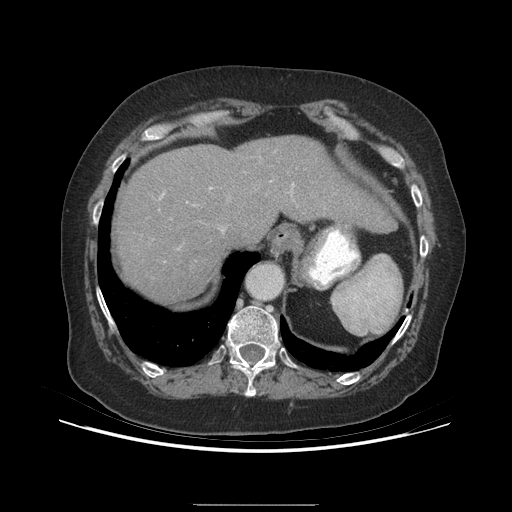
Contrast-enhanced abdominal CT (liver protocol), one axial slice. Slice 173 of 192 in the series (ordered by position). Reconstruction kernel STANDARD. 140 kVp. Soft-tissue window (W 400 / L 40 HU). 2.5 mm slice thickness. 512 × 512 image matrix. From the clinical record (not read from this slice): diagnosis: hepatocellular carcinoma (patient treated with transarterial chemoembolisation; whether this scan precedes or follows treatment is not stated here); TNM stage (as recorded): Stage-I; Child-Pugh class: A; tumour differentiation: moderately differentiated; tumour size: 3.2 cm.
Structures marked on this image (semi-automatically segmented with operator editing):
- liver parenchyma outside the tumour (the mass and vessels are separate outlines, so this box may not span the whole liver): bounding box [x1, y1, x2, y2] px = [114, 136, 394, 302]